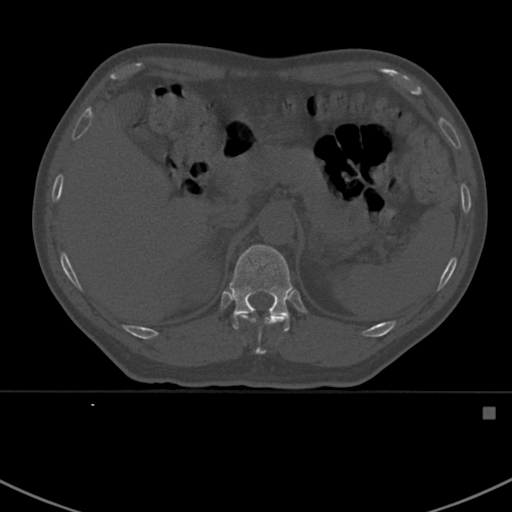
CT including the spine, one axial slice; reconstruction kernel Br40s; bone window (W 1800 / L 400 HU); 1.5 mm slice thickness; 512 × 512 image matrix. Patient: male, 59 years. From the clinical record (not read from this slice): primary cancer: prostate.
Annotated regions visible in this slice (semi-automatically segmented with operator editing):
- T11 vertebra: box from (x=238, y=315) to (x=284, y=355) px
- T12 vertebra: (x=229, y=245)–(x=293, y=332)